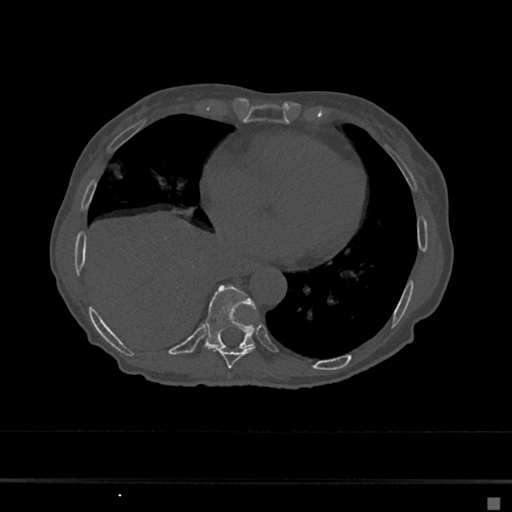
CT including the spine, one axial slice; slice 298 of 797 in the series (ordered by position); reconstruction kernel Br40s/3; bone window (W 1800 / L 400 HU); 0.5 mm slice thickness; 512 × 512 image matrix. Patient: female, 68 years. Case-level facts recorded for this patient, not image findings: primary cancer: renal.
Annotated regions visible in this slice (semi-automatically segmented with operator editing):
- T8 vertebra: box from (x=213, y=347) to (x=256, y=369) px
- T9 vertebra: (x=203, y=285)–(x=256, y=349)